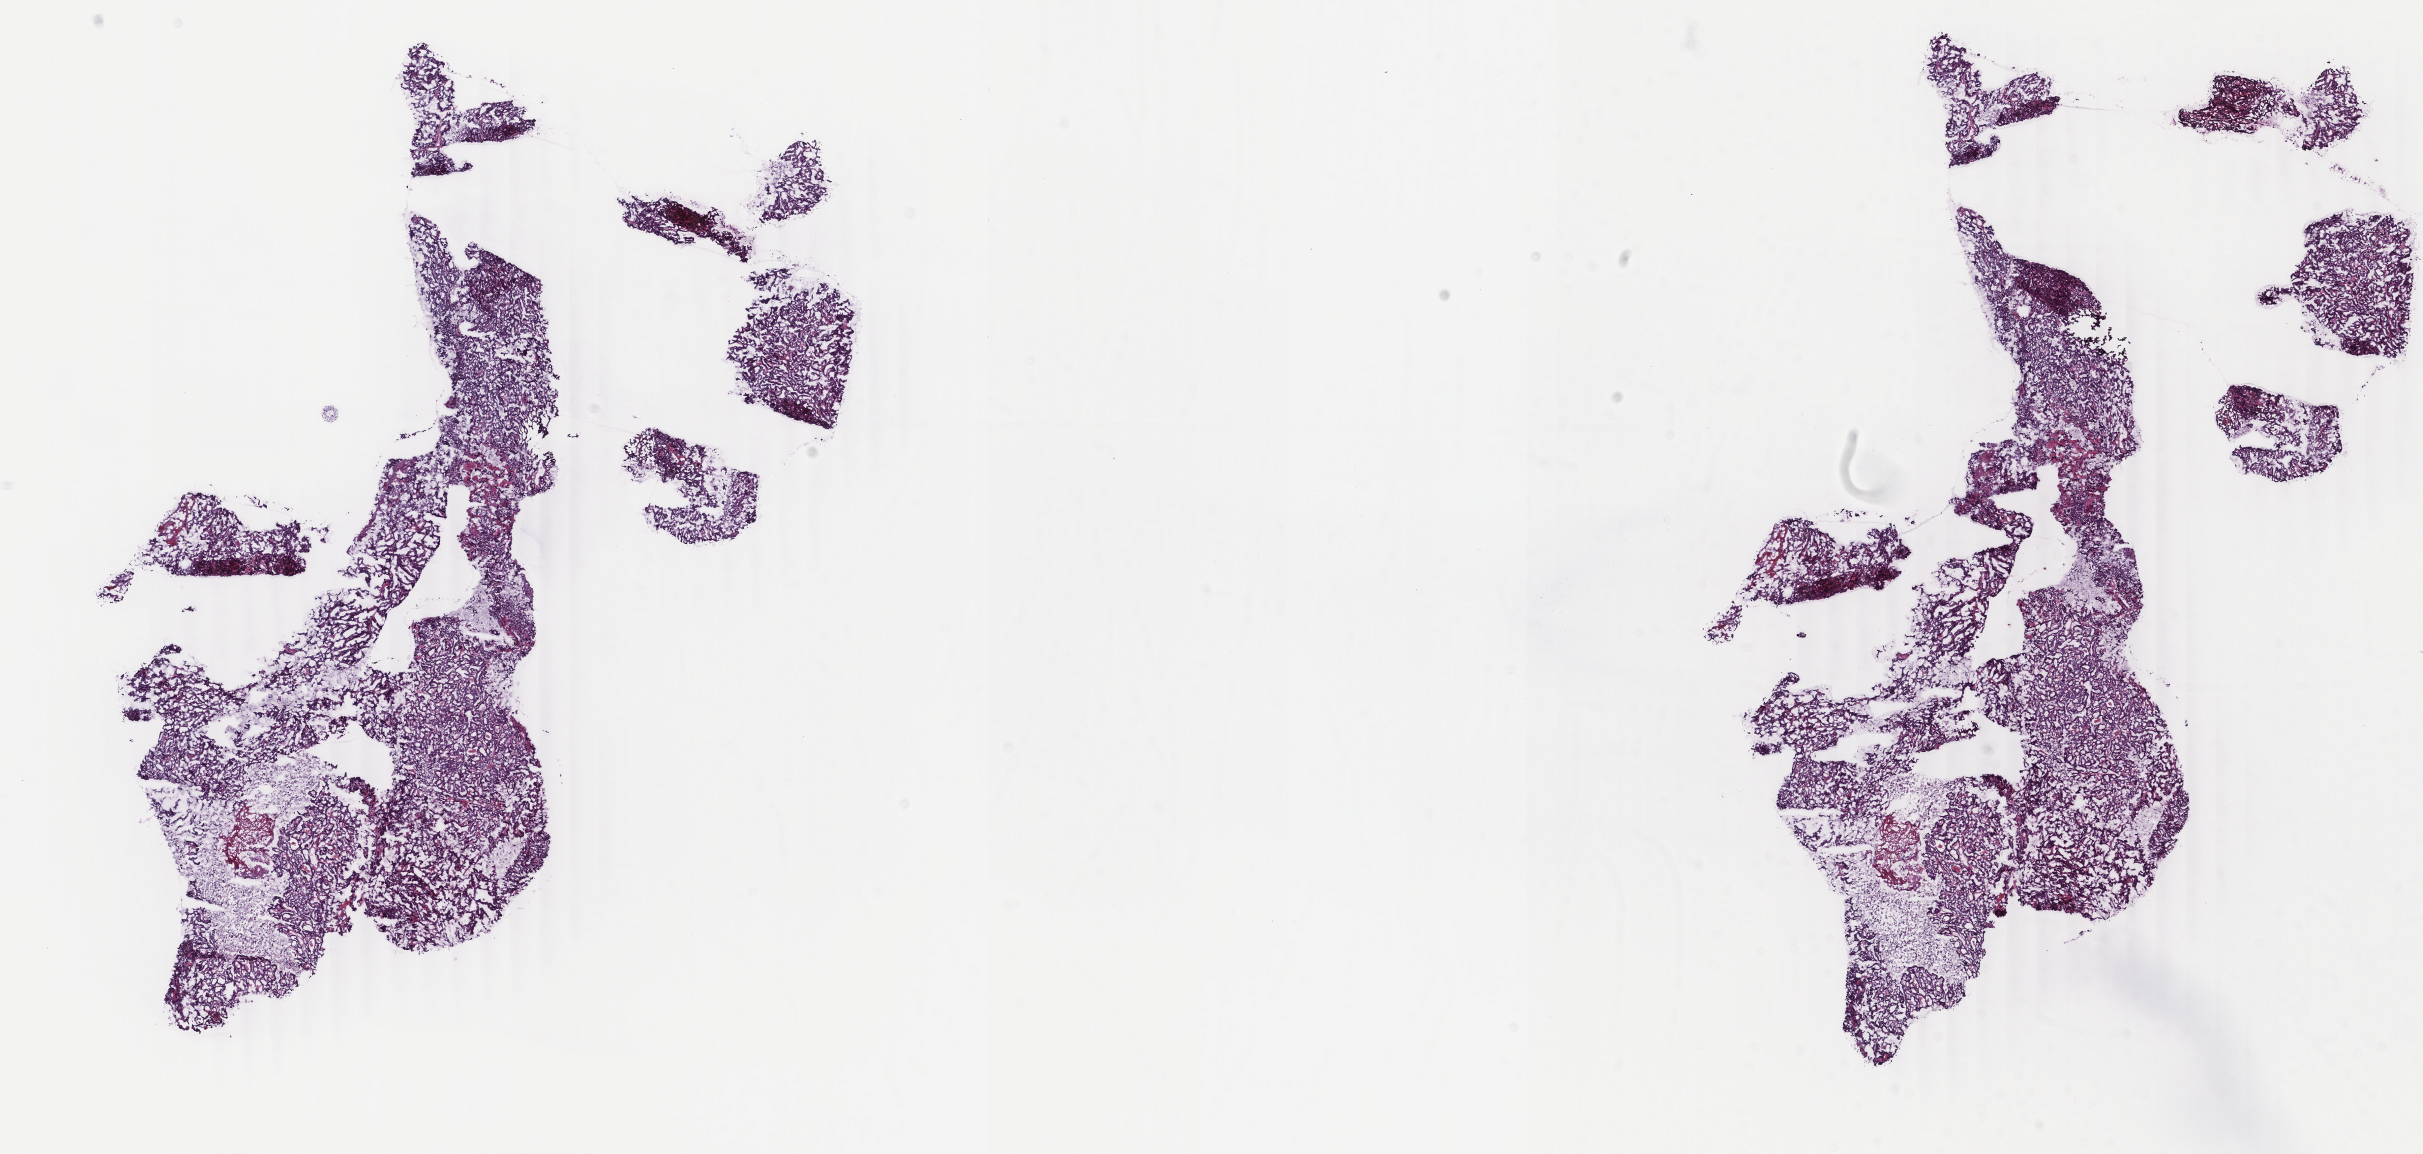
Digitized H&E-stained tissue section (whole slide) — low-resolution overview of the scanned area, about 19.3 x 9.2 mm (slide scanned at 40x); frozen section from the top of the tissue portion; primary tumour sample from the thyroid. Patient: male, age at initial diagnosis 75 years. Slide review estimates, as recorded: tumour cells 100%, tumour nuclei 90%, normal cells 0%, stromal cells 0%, necrosis 0%. Inflammatory infiltration, as recorded: lymphocyte infiltration 0%, monocyte infiltration 0%, neutrophil infiltration 0%.
Diagnosis: Papillary adenocarcinoma, NOS (thyroid gland). AJCC pathologic stage: IVA (7th edition). Laterality: left.